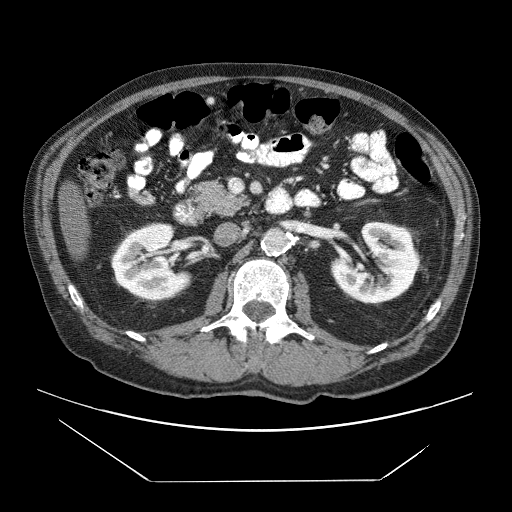
Contrast-enhanced abdominal CT (liver protocol), one axial slice. Position 11 of 83 along the scan axis. Soft-tissue window (W 400 / L 40 HU). 2.5 mm slice thickness. 512 × 512 image matrix. From the clinical record (not read from this slice): diagnosis: hepatocellular carcinoma (patient treated with transarterial chemoembolisation; whether this scan precedes or follows treatment is not stated here); TNM stage (as recorded): Stage-IVB; Child-Pugh class: B; tumour differentiation: poorly differentiated; tumour nodularity: uninodular.
Outlined on this slice (semi-automatically segmented with operator editing):
- liver parenchyma outside the tumour (the mass and vessels are separate outlines, so this box may not span the whole liver): bounding box [x1, y1, x2, y2] px = [58, 184, 90, 260]